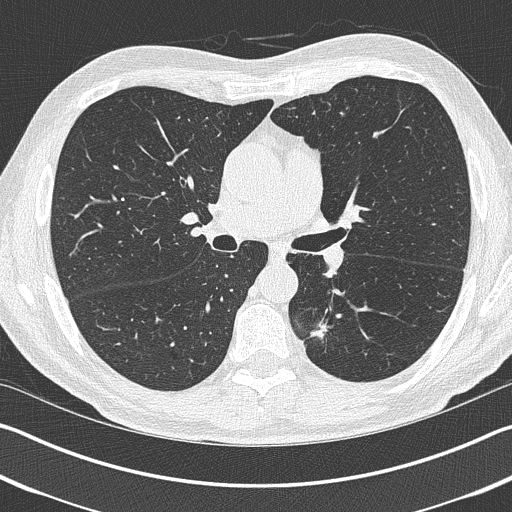
Low-dose screening chest CT, one axial slice. Position 243 of 402 along the scan axis. Reconstruction kernel B50f. Lung window (W 1500 / L -600 HU). 1 mm slice thickness. 512 × 512 image matrix, field of view 340 × 340 mm.
Annotated regions visible in this slice (manually delineated by an expert):
- lesion 1 (tumor, lower lobe of left lung): bounding box <310,321,330,340> (left, top, right, bottom; pixels)